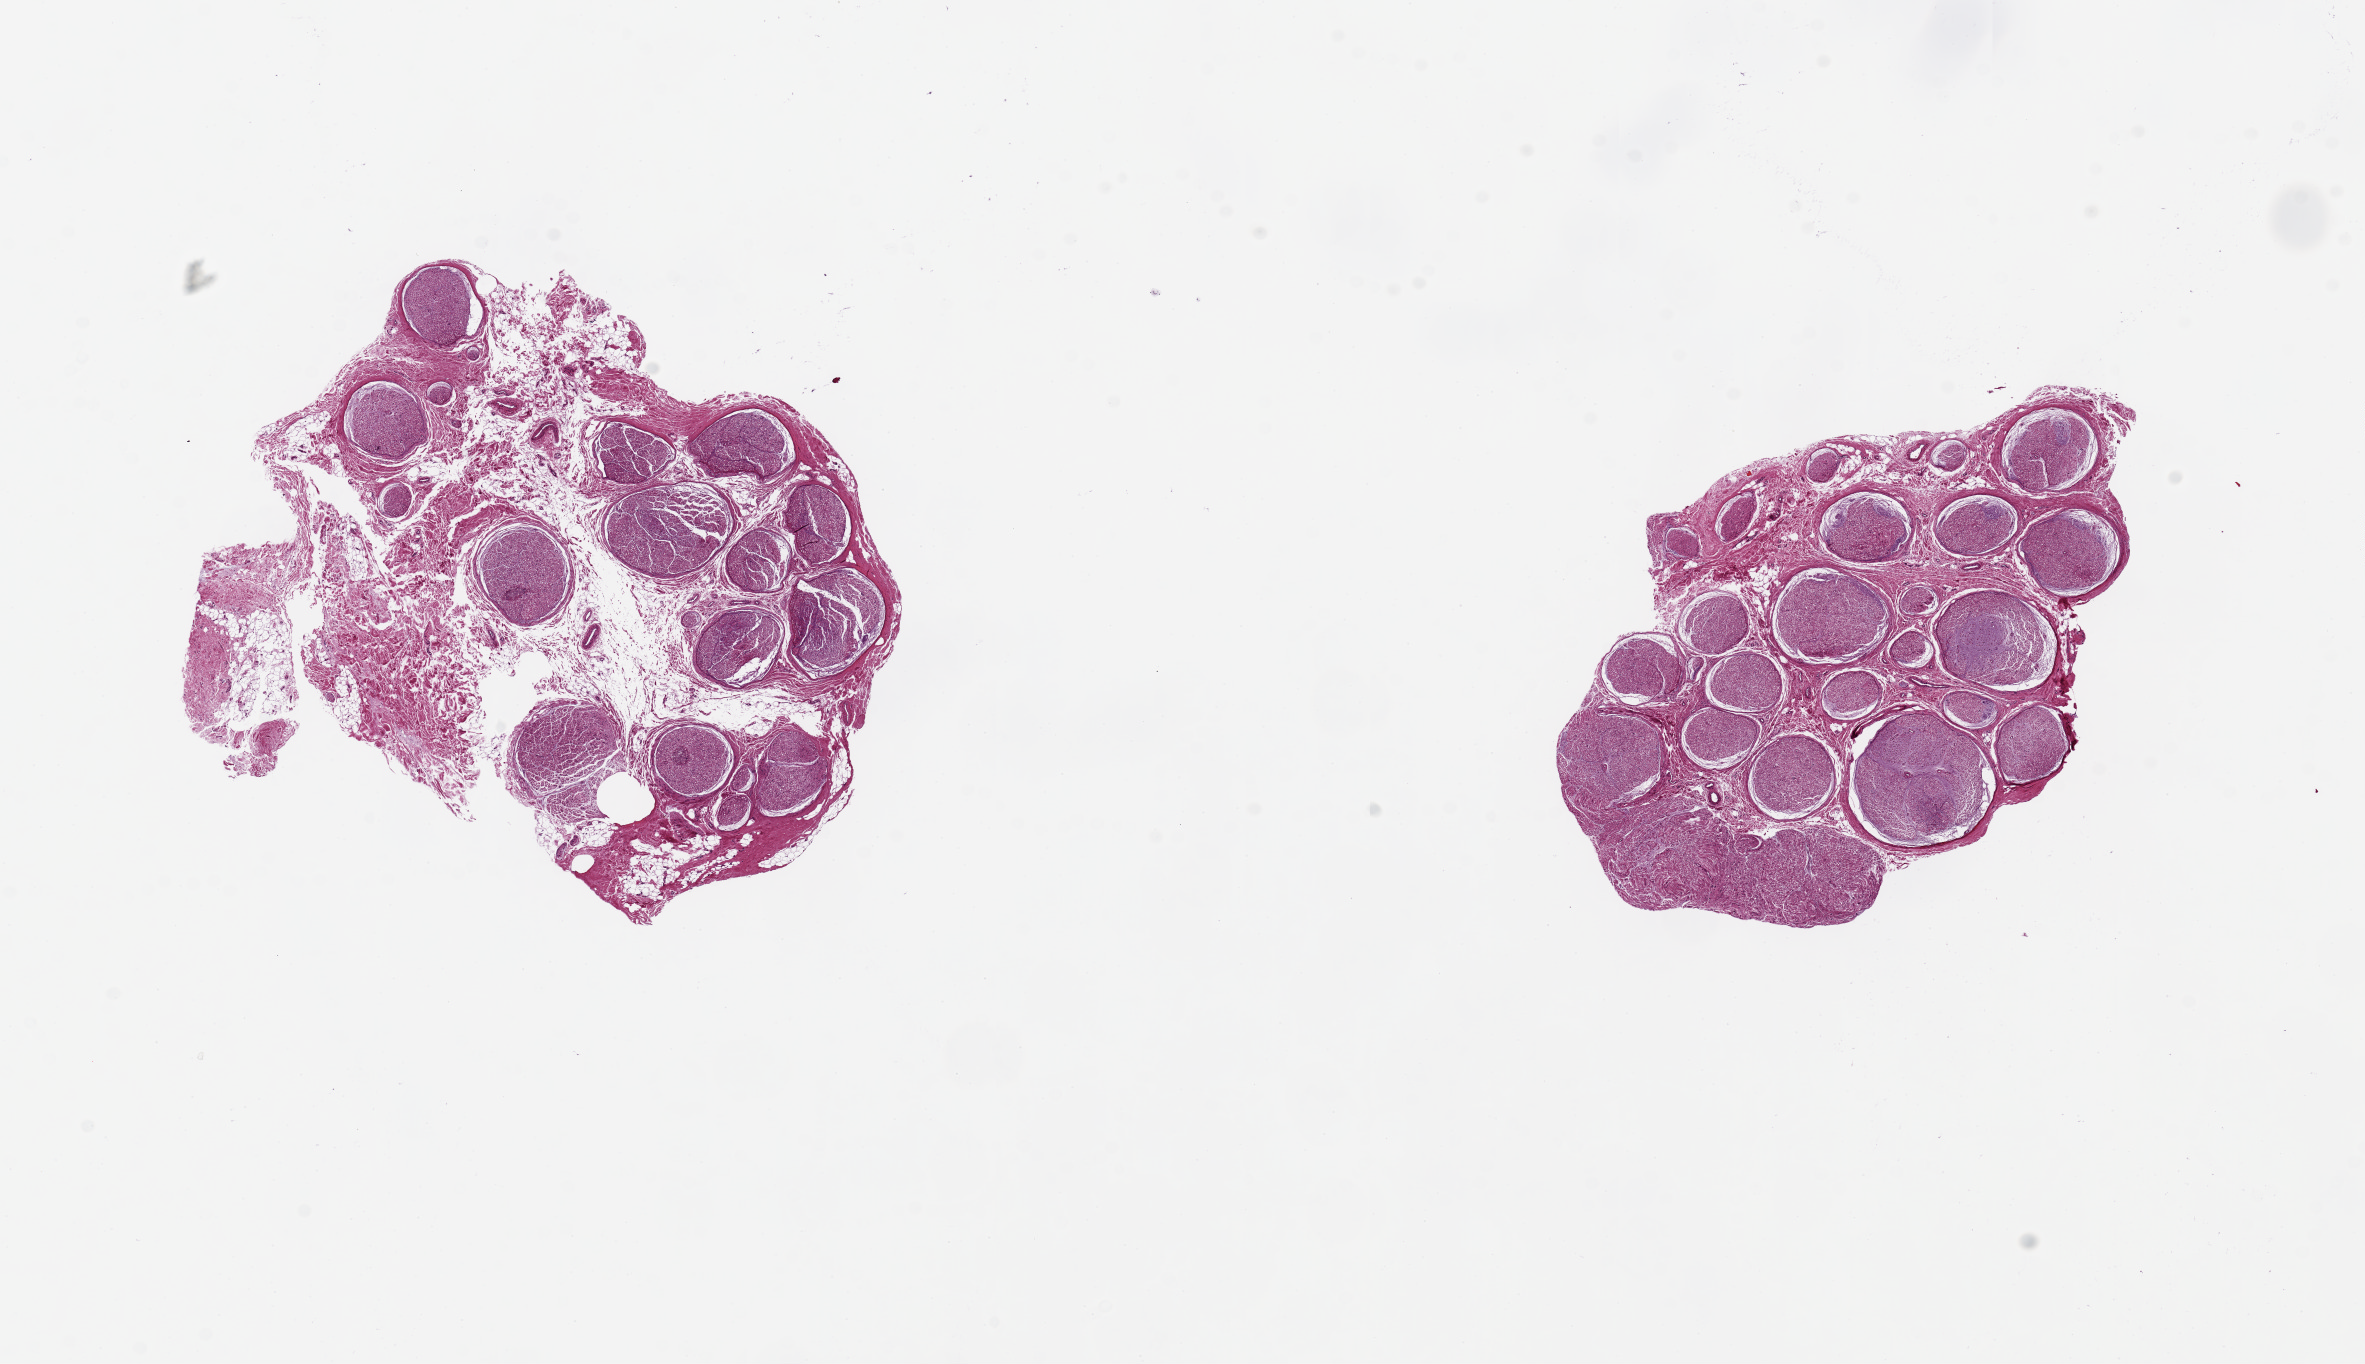
Haematoxylin and eosin whole-slide image — a low-resolution overview of the entire scanned area, about 18.7 x 10.8 mm (slide scanned at 20x); PAXgene-fixed paraffin-embedded (PFPE) section; section of tibial nerve (target tissue); tissue donor sample.
* reviewer comment on this tissue sample: 2 pieces, 5x5 & 6x3mm; 1 has 20% stroma, mainly on edges